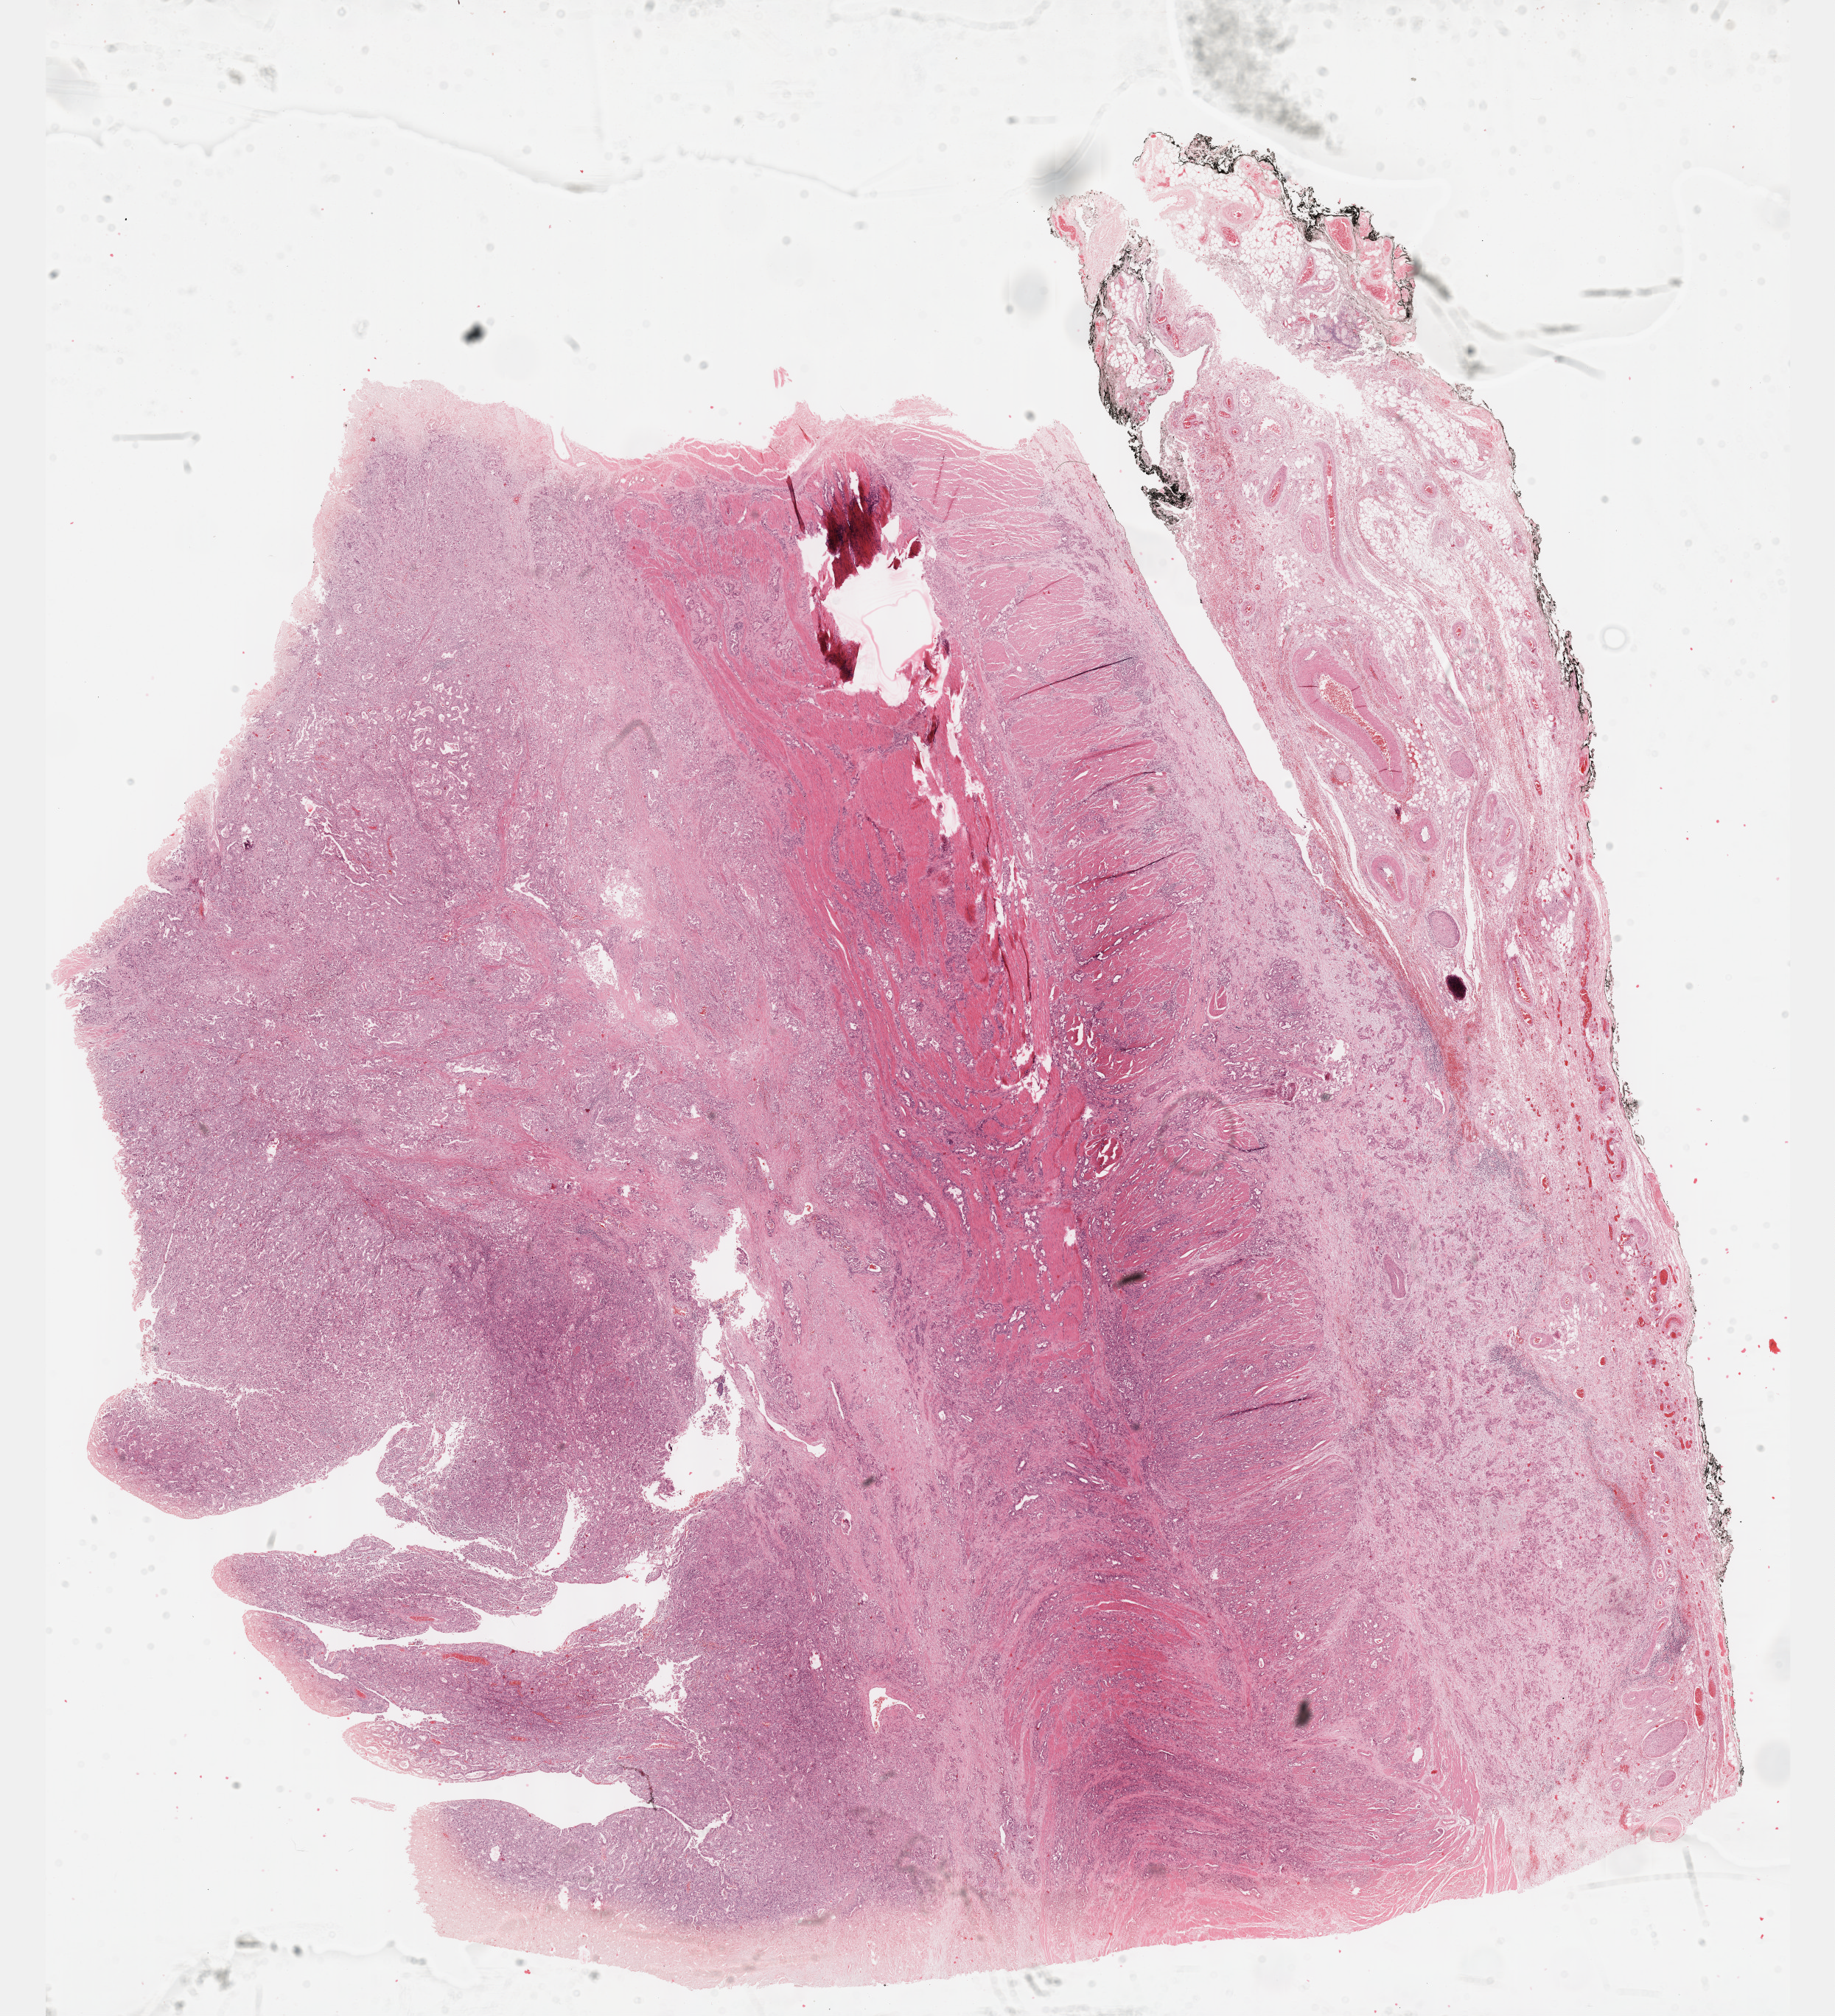
H&E whole-slide image — a low-resolution overview of the entire scanned area, about 20.1 x 22.1 mm; FFPE section; esophagus, primary tumour sample. Male, age 43 years at initial diagnosis. Histologic grade: G3 (poorly differentiated).
- AJCC pathologic stage: III
- diagnosis: Adenocarcinoma, NOS (lower third of esophagus)